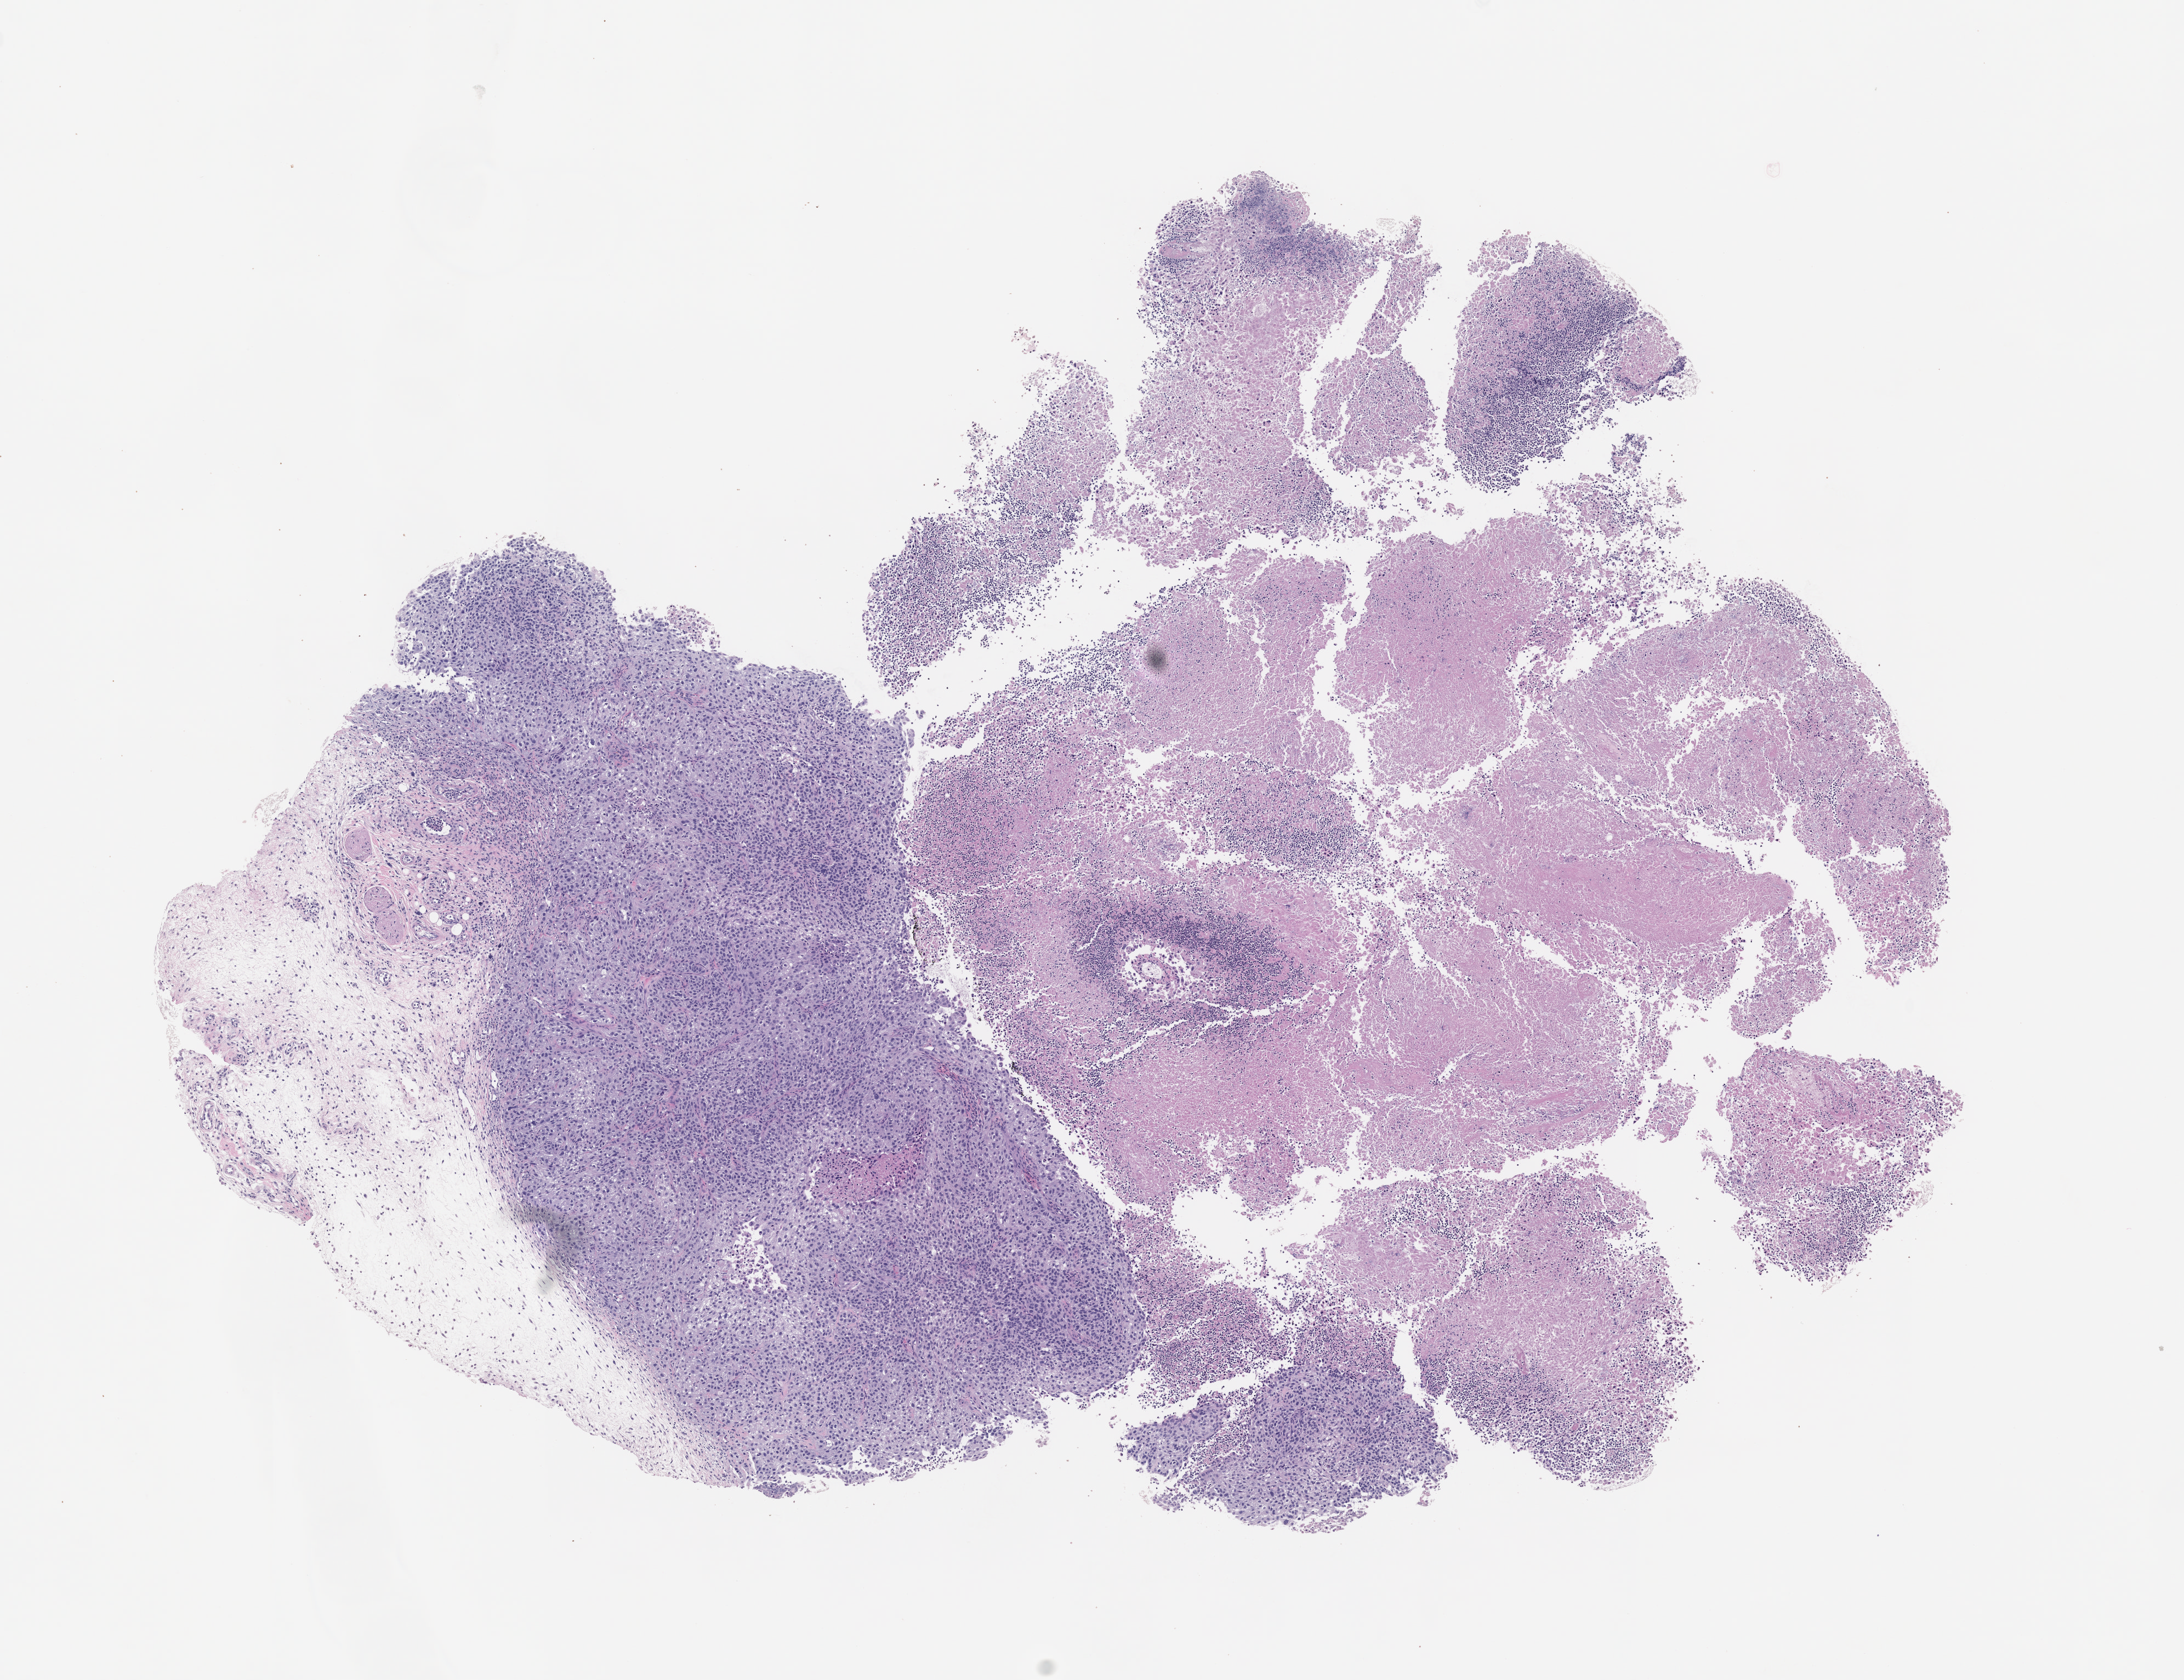
Whole-slide image, hematoxylin and eosin (H&E): patient-derived xenograft (human tumor grown in a mouse), passage 3 — low-resolution overview of the scanned area, about 8.0 x 6.2 mm. FFPE section. Tumor site category: bladder.
Originating patient diagnosis: Transitional Cell Carcinoma.